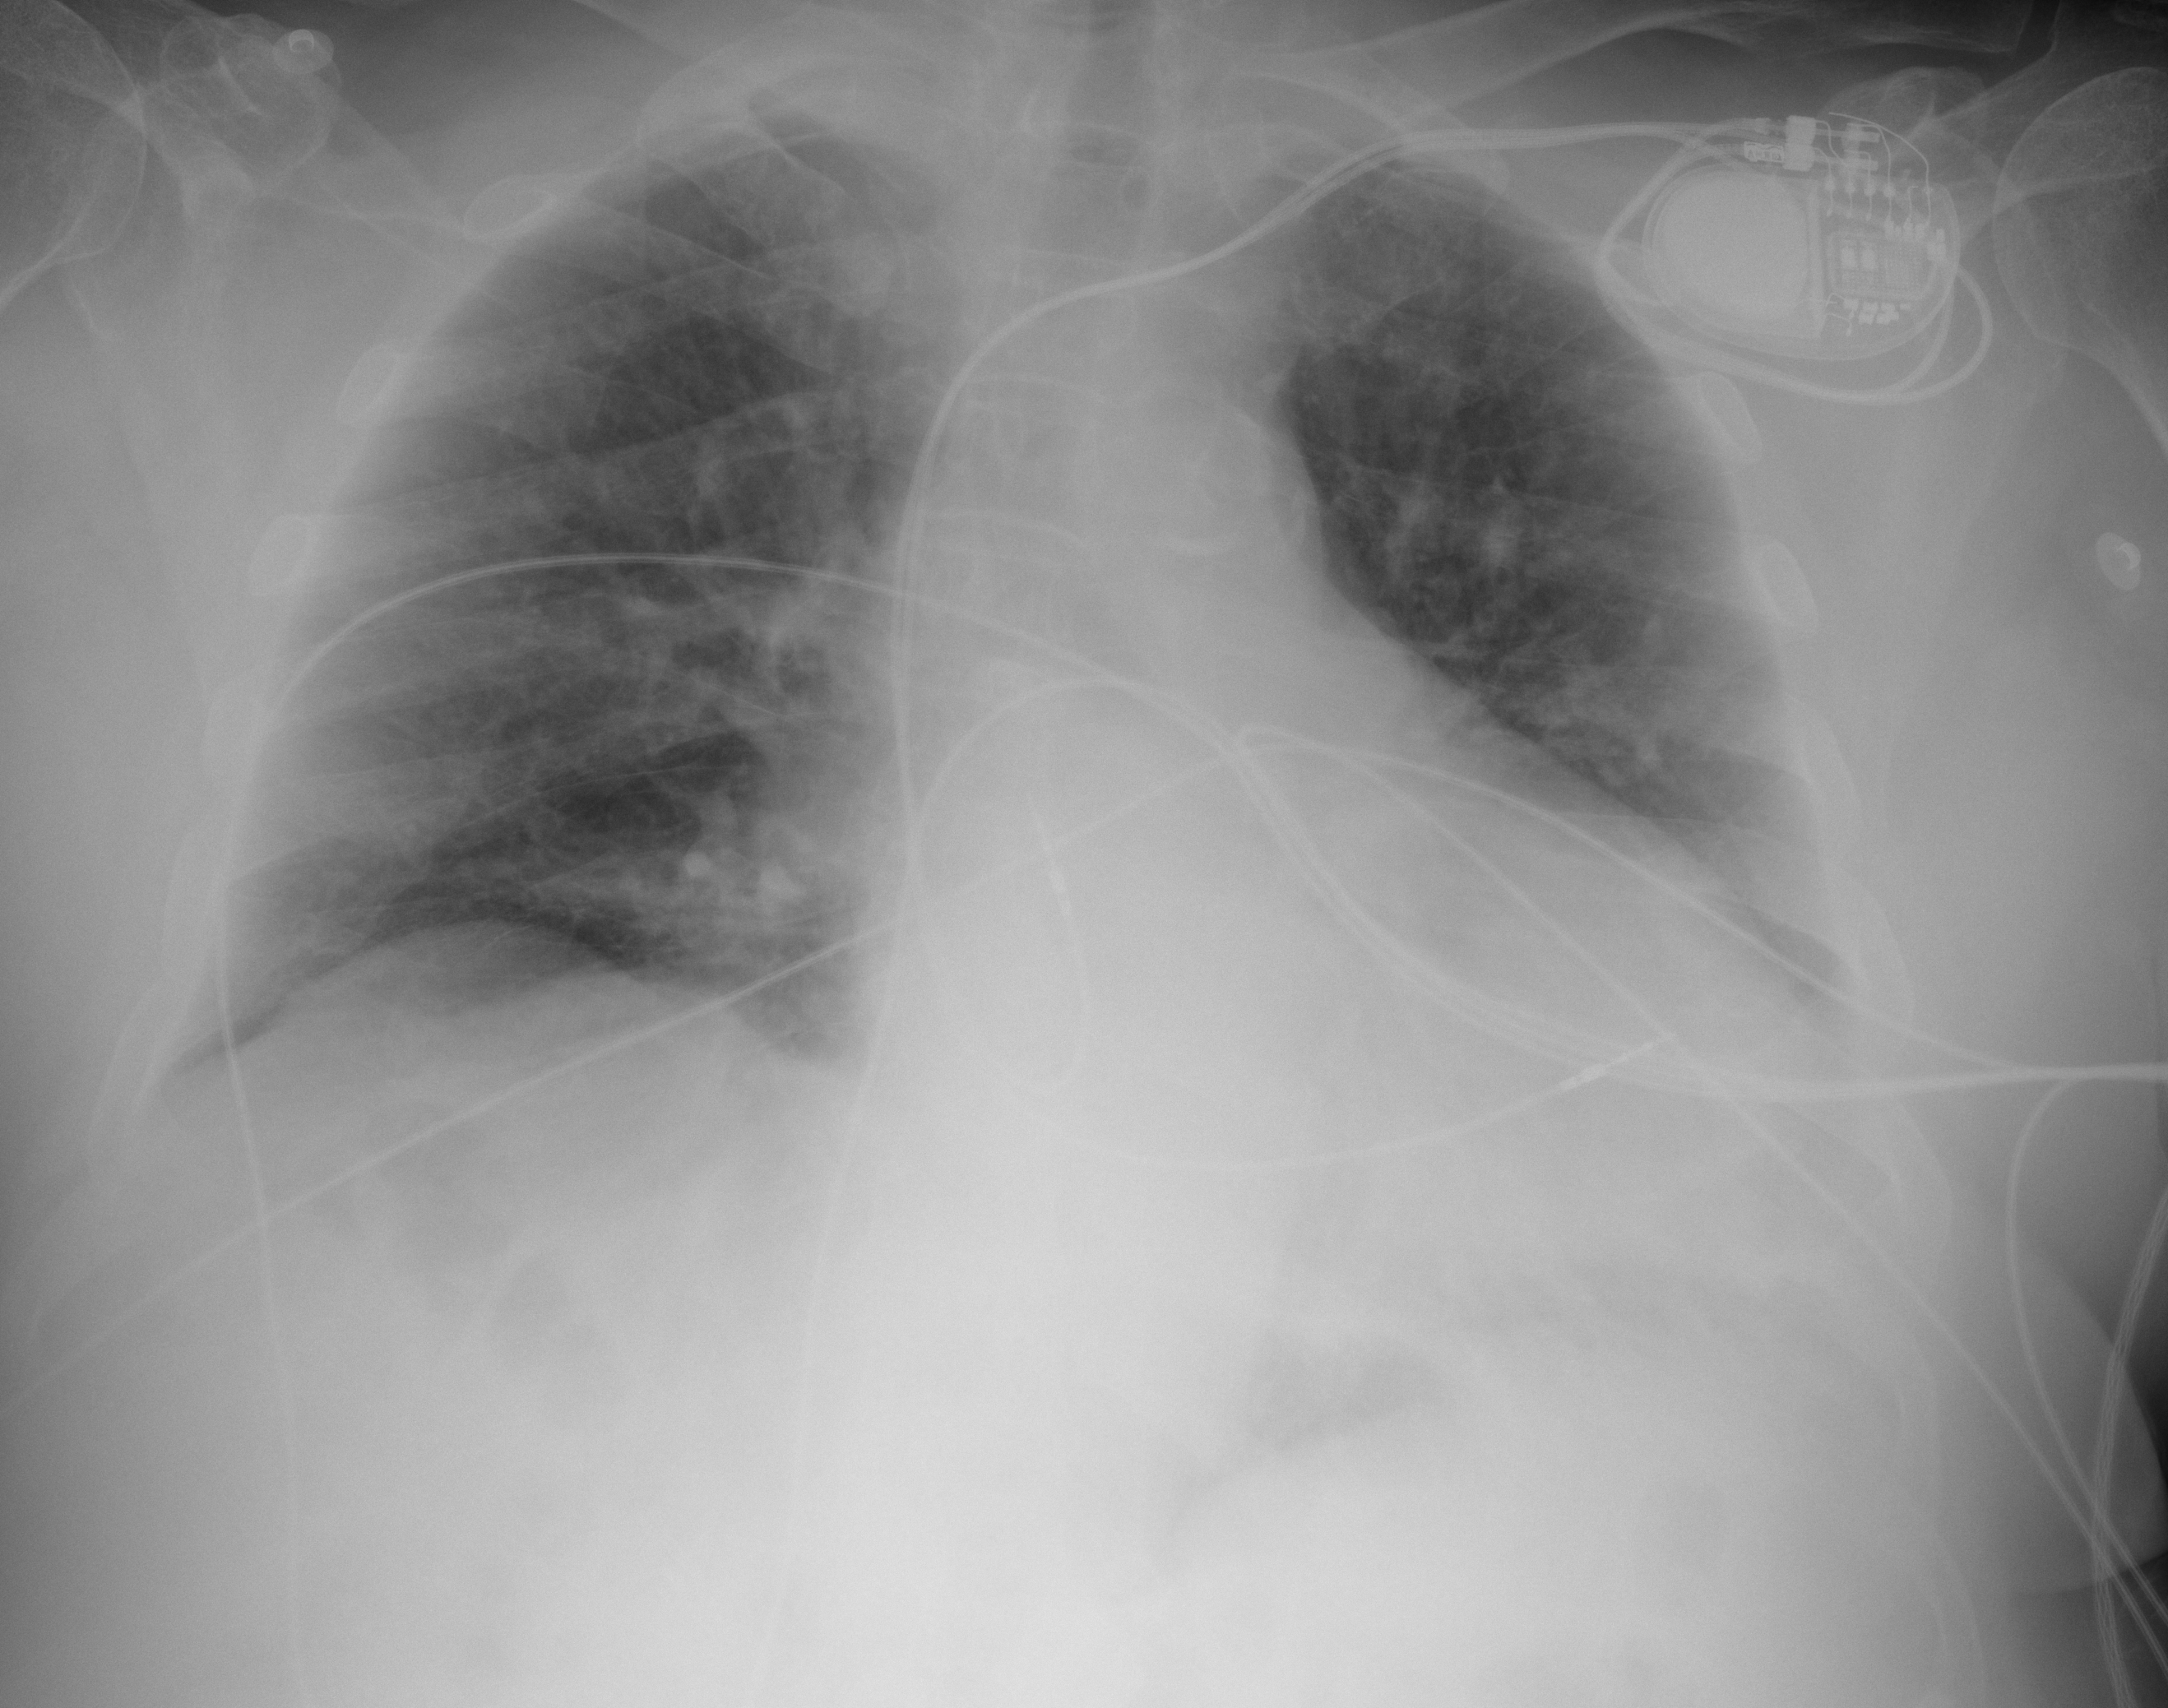
Chest X-ray (portable), AP projection. Male patient, age 88 years; imaged 0 days after the COVID-19 diagnosis.
Key findings recorded by the radiologist: Right lung is low in volume but otherwise clear of significant consolidation.